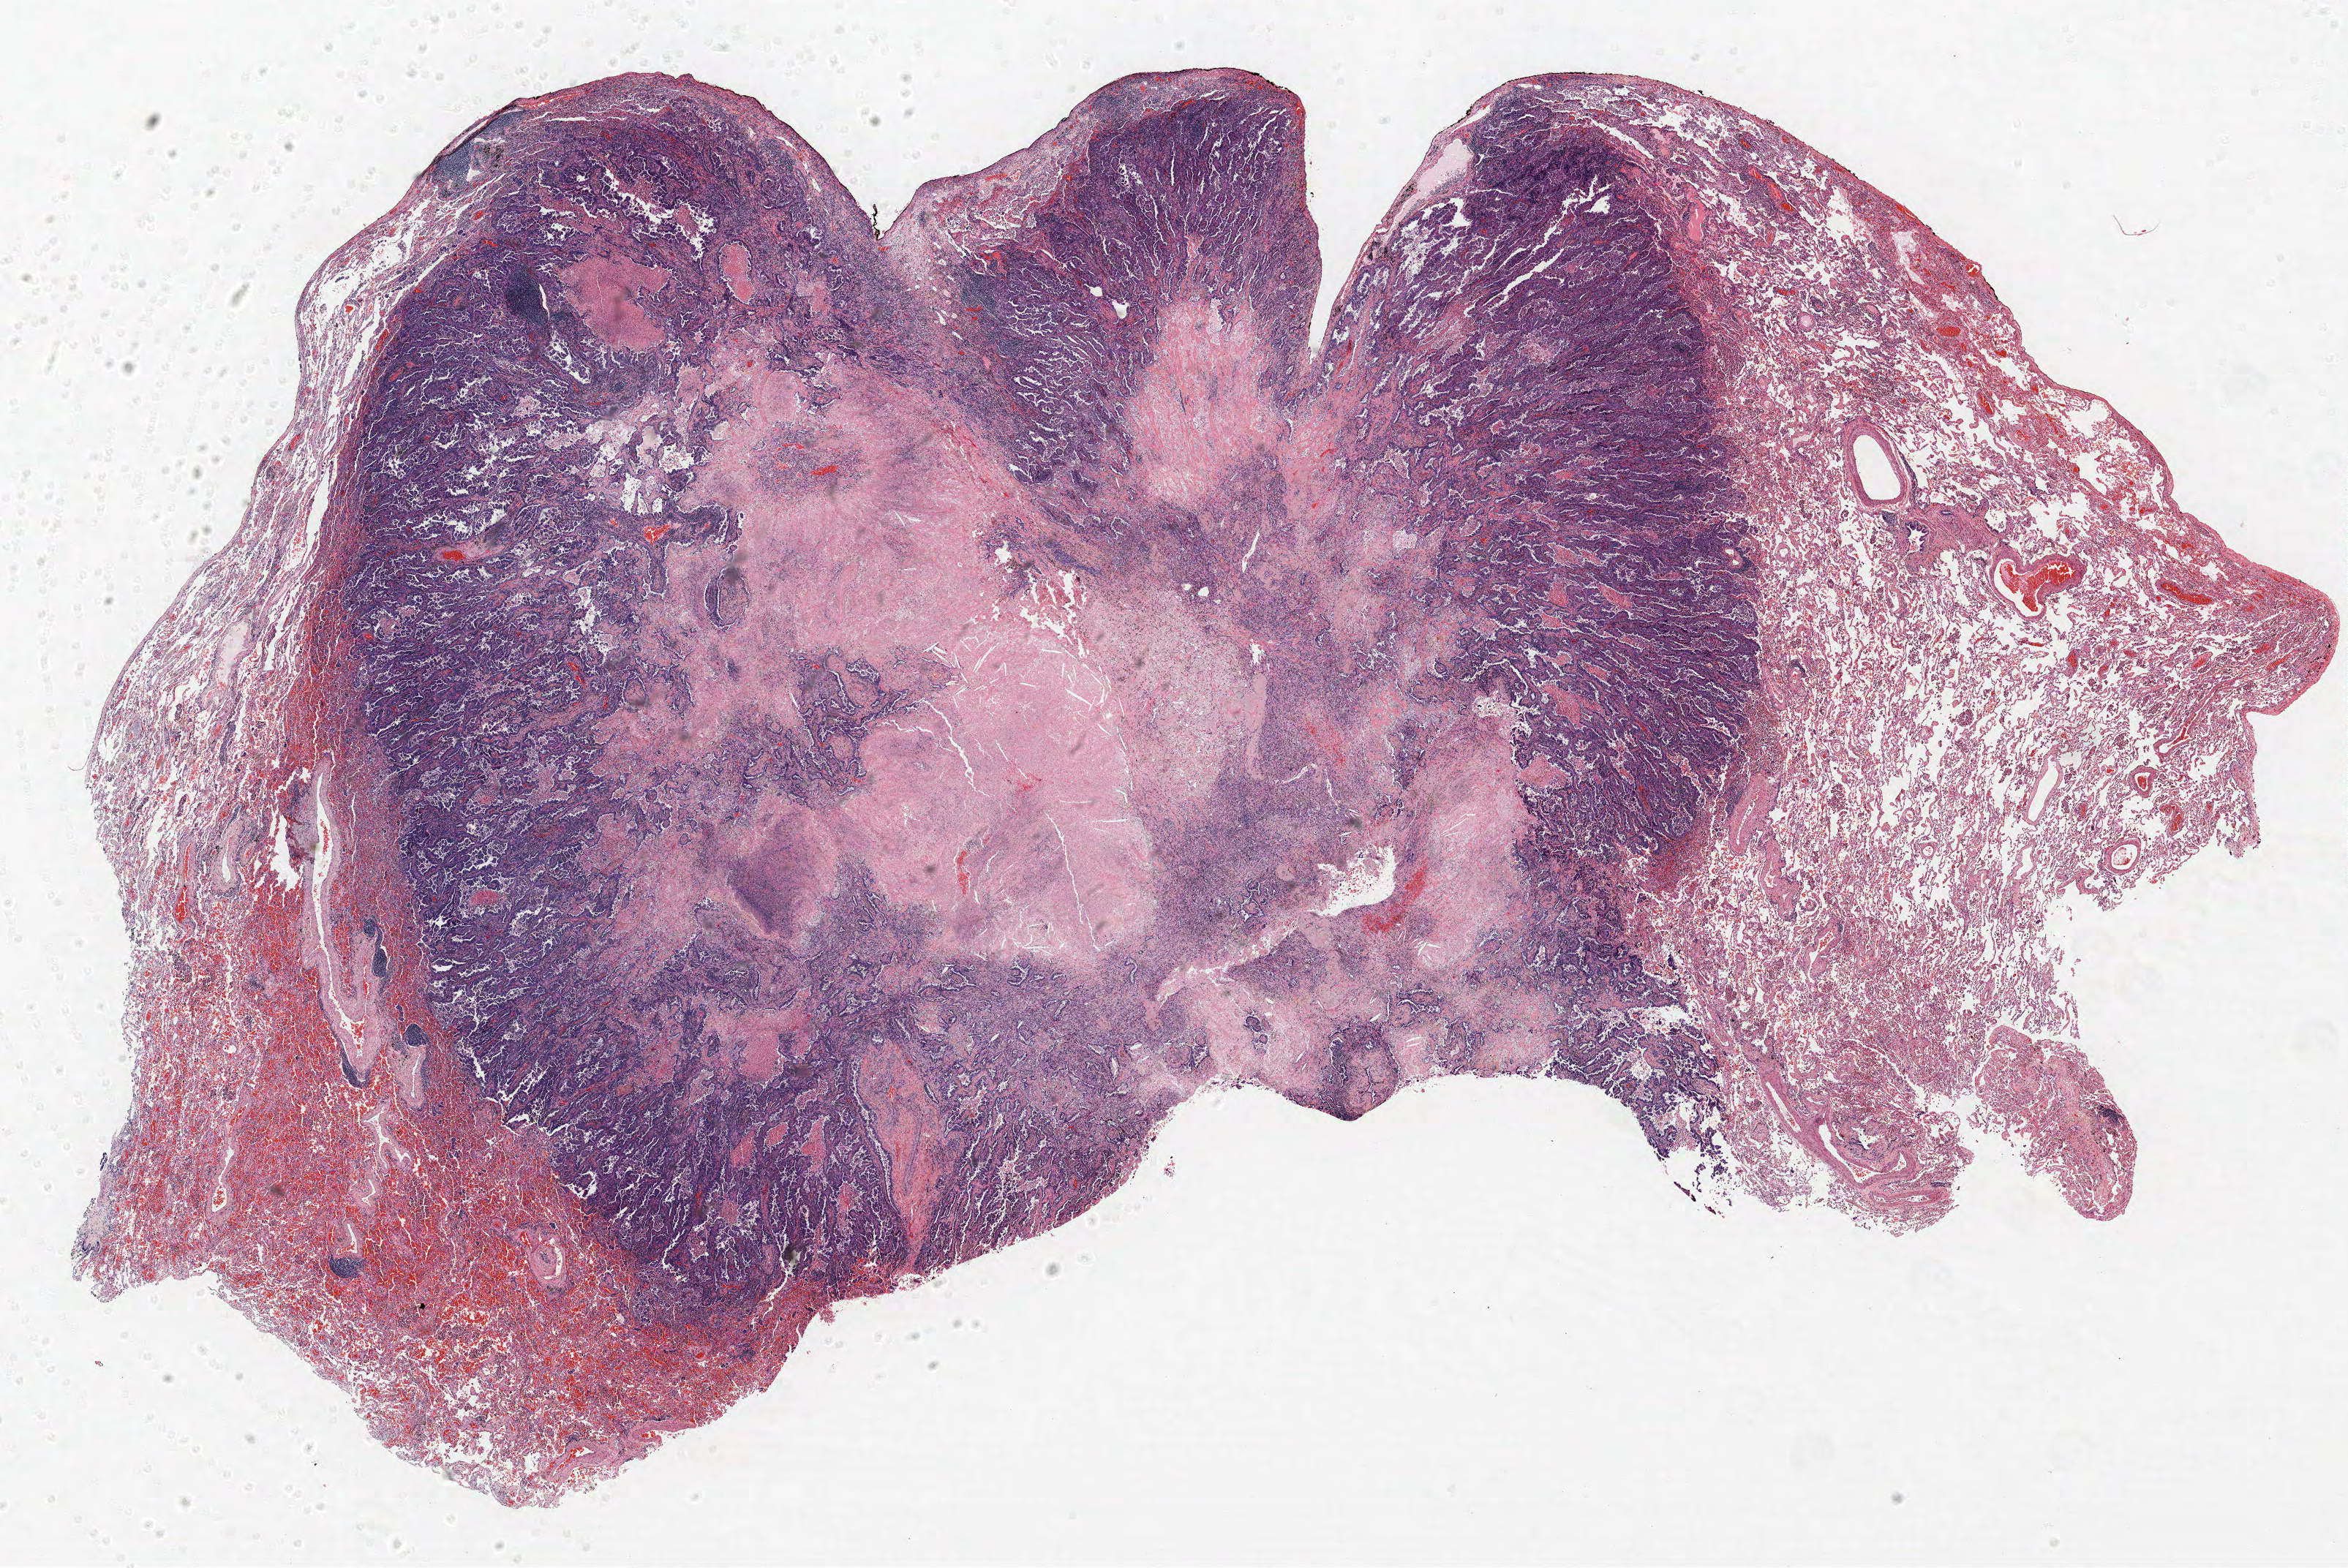
H&E whole-slide image, a low-resolution overview of the entire scanned area, about 25.7 x 17.2 mm; FFPE section; lung tissue. Male patient, aged 70 at enrolment. Current smoker at enrolment.
• primary tumour location (clinical record): left upper lobe
• stage (AJCC 6th edition): IIIB
• participant's lung-cancer diagnosis: Bronchiolo-alveolar adenocarcinoma, NOS (ICD-O-3 8250/3)
• tumour size (pathology): 25 mm